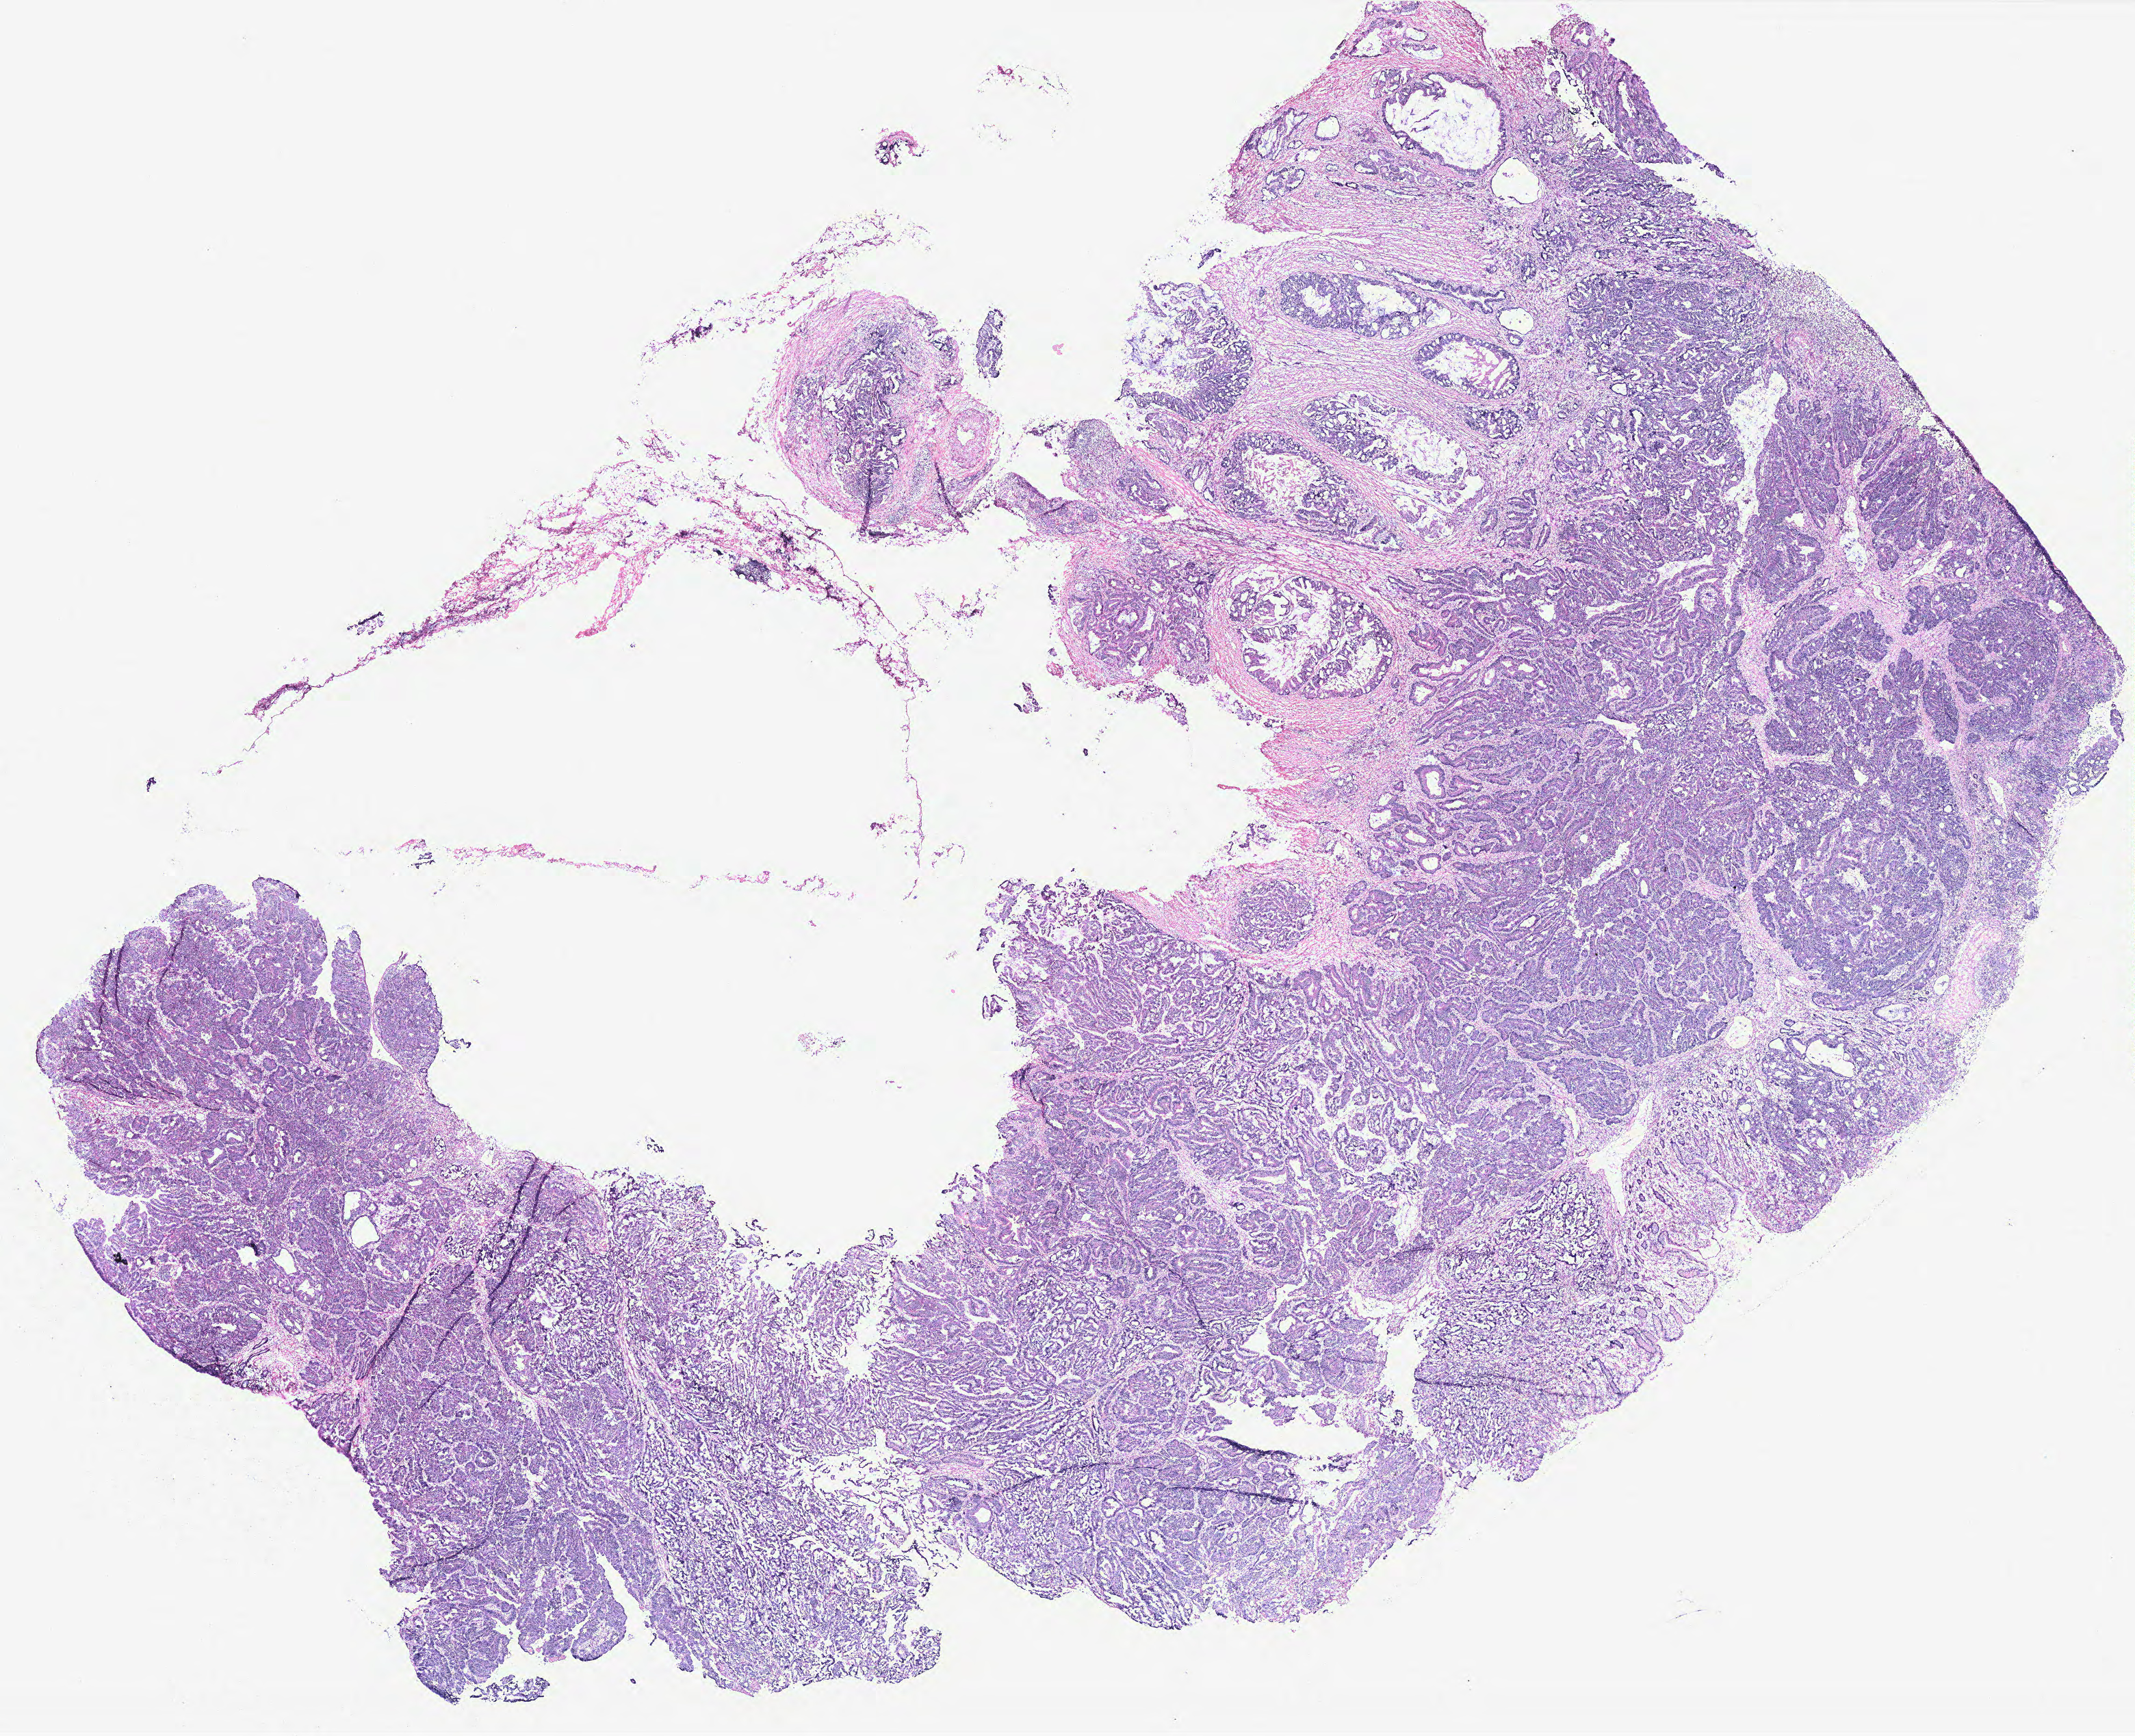
Digitized Hematoxylin and eosin (H&E) stained tissue section (whole slide), low-resolution overview of the scanned area, about 25.0 x 20.3 mm, colon, tissue type not recorded.
Patient diagnosis (cohort enrolment): colon cancer (colon).